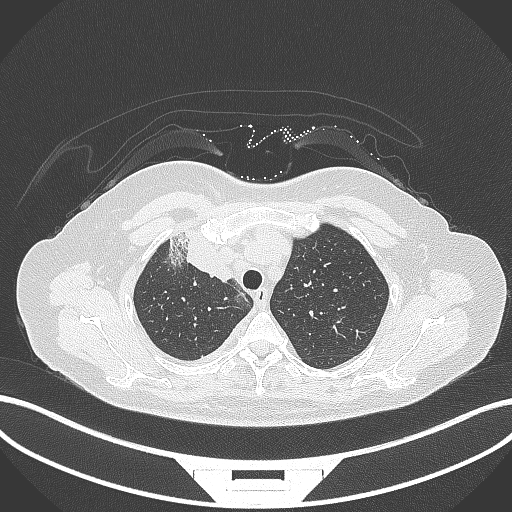
Chest CT, one axial slice; 120 kVp; lung window (W 1500 / L -600 HU); 512 × 512 image matrix. Patient: female, 52 years. Case-level facts recorded for this patient, not image findings: clinical TNM (as recorded): T3 N1 M1.
Outlined on this slice (rectangle marked by the reading radiologist):
- lung tumour (recorded histology: adenocarcinoma): box from (x=168, y=233) to (x=237, y=282) px